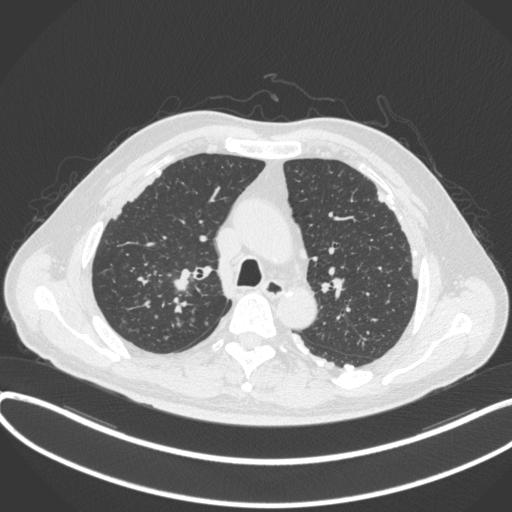
Chest CT, one axial slice. Slice 296 of 455 in the series (ordered by position). 120 kVp. Lung window (W 1500 / L -600 HU). 1 mm slice thickness. 512 × 512 image matrix, field of view 400 × 400 mm. Patient: male, 58 years. Case-level facts recorded for this patient, not image findings: clinical TNM (as recorded): T1c N0 M0.
Annotated regions visible in this slice (rectangle marked by the reading radiologist):
- lung tumour (recorded histology: squamous cell carcinoma): bounding box <164,267,200,302> (left, top, right, bottom; pixels)